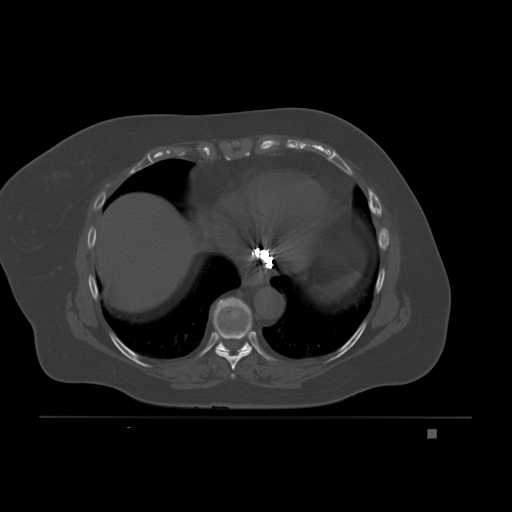
CT including the spine, one axial slice. Slice 115 of 221 in the series (ordered by position). Bone window (W 1800 / L 400 HU). 3 mm slice thickness. 512 × 512 image matrix. Patient: female, 63 years. Case-level facts recorded for this patient, not image findings: primary cancer: breast.
Structures marked on this image (semi-automatically segmented with operator editing):
- T7 vertebra: bounding box (x1, y1, x2, y2) in pixels: (230, 374, 235, 378)
- T8 vertebra: (215, 328, 252, 370)
- T9 vertebra: (213, 297, 252, 353)